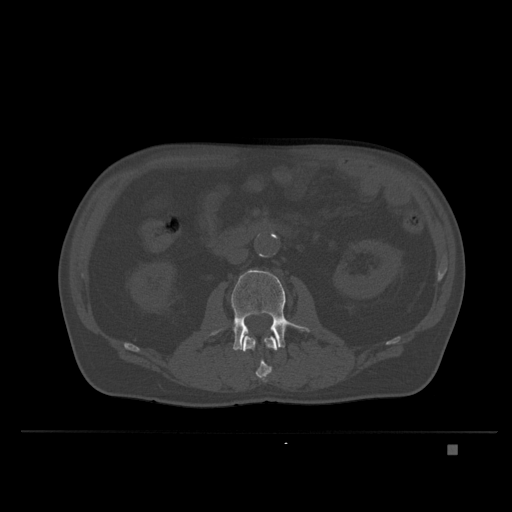
CT including the spine, one axial slice. Slice 104 of 435 in the series (ordered by position). Bone window (W 1800 / L 400 HU). 1.5 mm slice thickness. 512 × 512 image matrix, field of view 434 × 434 mm. Patient: male, 73 years. Case-level facts recorded for this patient, not image findings: primary cancer: skin.
Outlined on this slice (semi-automatic segmentation, software-assisted and operator-edited):
- L2 vertebra: bounding box <242,333,279,383> (left, top, right, bottom; pixels)
- L3 vertebra: <211,269,310,351>